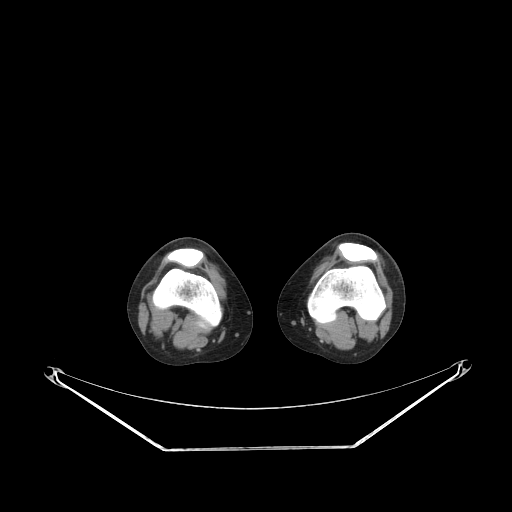
CT of an extremity soft-tissue mass (from a PET/CT study), one axial slice; position 165 of 223 along the scan axis; reconstruction kernel STANDARD; 140 kVp; soft-tissue window (W 400 / L 40 HU); 3.75 mm slice thickness; 512 × 512 image matrix, field of view 500 × 500 mm. Female patient. Case-level facts recorded for this patient, not image findings: histological type: spindle cell suggestive of biphasic synovial sarcoma; grade: intermediate; site of the primary tumour: left knee.
Structures marked on this image (expert contour drawn on MRI and transferred to this co-registered scan by the dataset authors):
- gross tumour volume including surrounding oedema: bounding box (x1, y1, x2, y2) in pixels: (377, 276, 389, 298)
- gross tumour volume (mass): (377, 276, 389, 296)